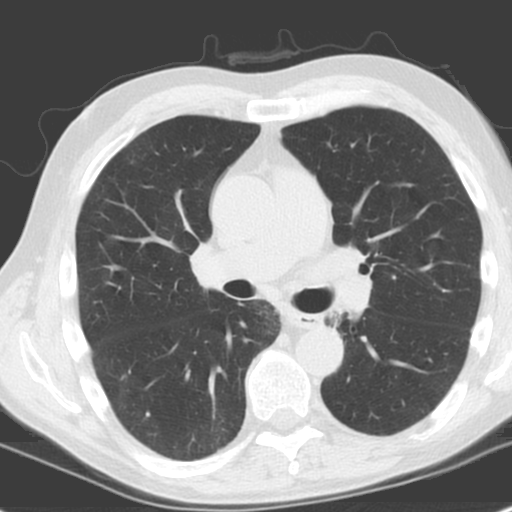
Axial slice from a low-dose chest CT screening exam, first (baseline) screen, lung window (W 1500 / L -600 HU), 3.2 mm slice thickness, slice 78 of 185 in the series, 512 × 512 image matrix, field of view 321 × 321 mm. Male, age 61 years at enrolment. Former smoker at enrolment.
Expert-annotated lung lesion, bounding box [x1, y1, x2, y2] px = [310, 304, 356, 342]. Screening reader's record for this exam: no non-calcified nodule ≥4 mm recorded. Official screen result: negative screen, minor abnormalities not suspicious for lung cancer. Participant outcome: lung cancer diagnosed 1146 days after this screen (after the third annual screen) — squamous cell carcinoma, NOS, left upper lobe, left lower lobe, well differentiated (G1), stage IIB (AJCC 6th edition), 100 mm at pathology.